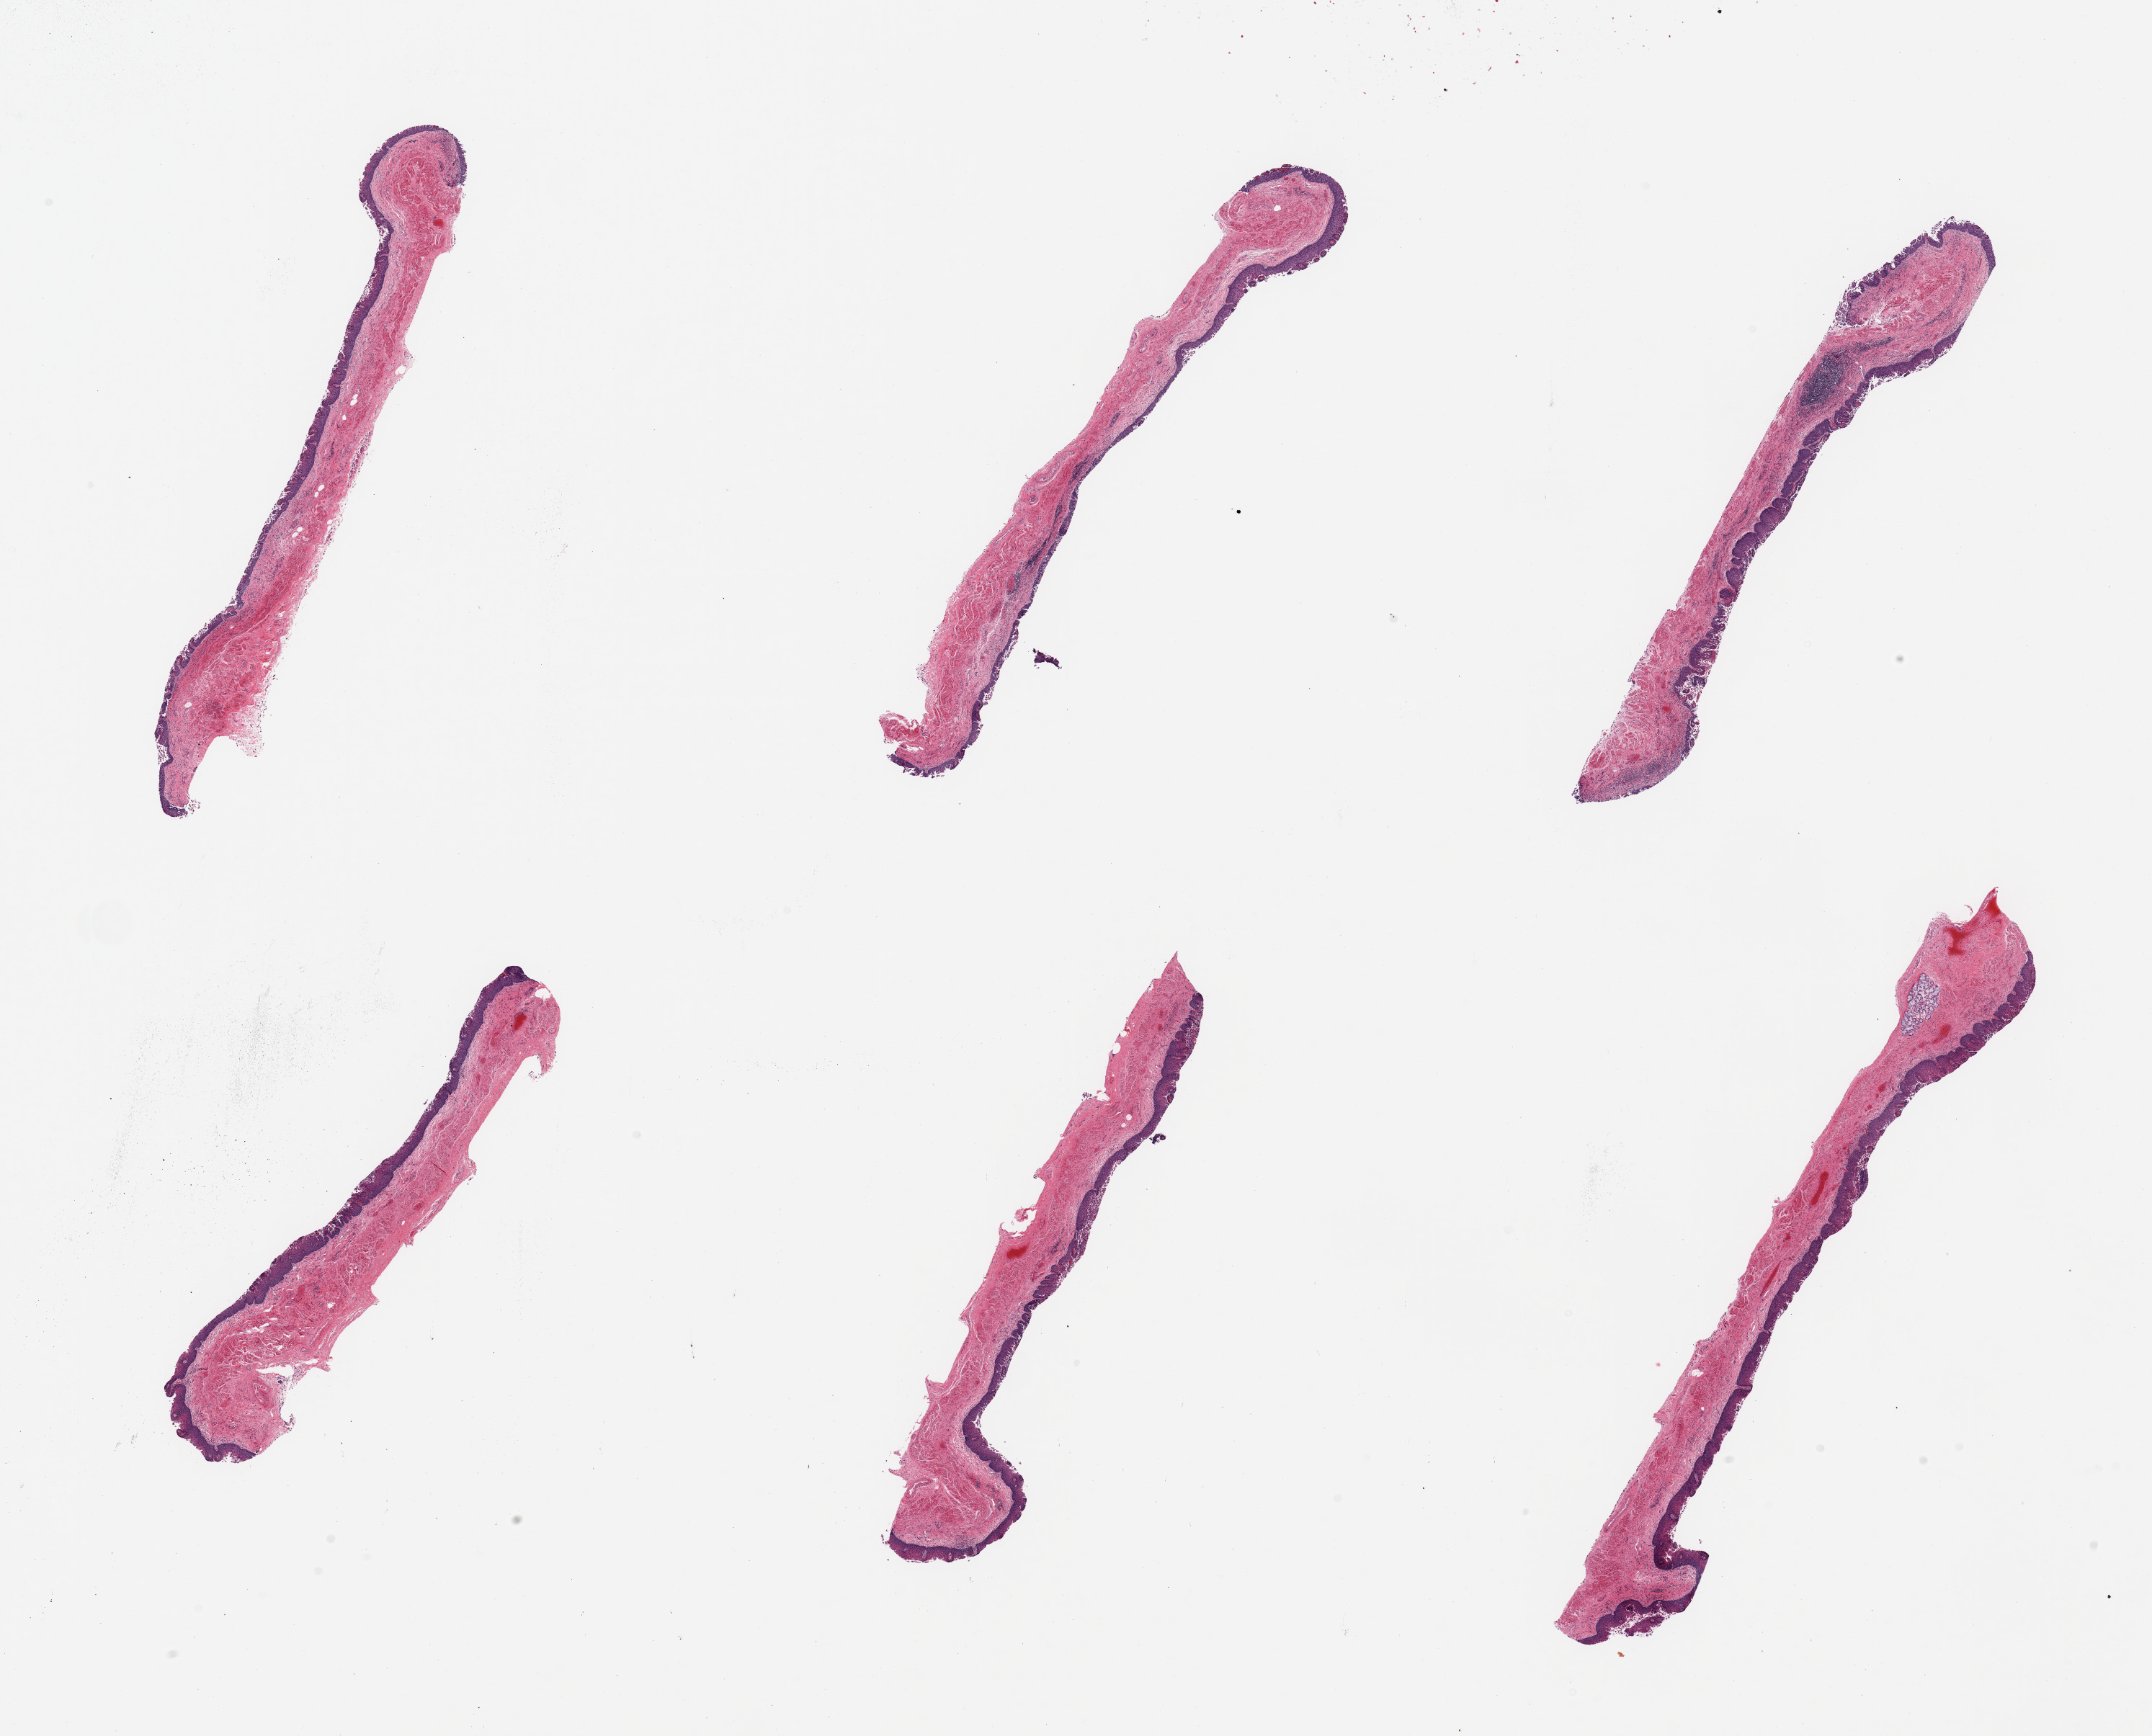
Digitized haematoxylin and eosin-stained section, brightfield, shown as a low-resolution overview of the whole scanned area (about 23.6 x 19.1 mm, slide scanned at 20x); PAXgene-fixed paraffin-embedded (PFPE) section; section of esophageal mucous membrane (target tissue); donor tissue sample. Male donor.
* reviewer comment on this tissue sample: 6 pieces, squamous mucosa up to ~0.2mm, partly sloughing, ~15-20% thickness